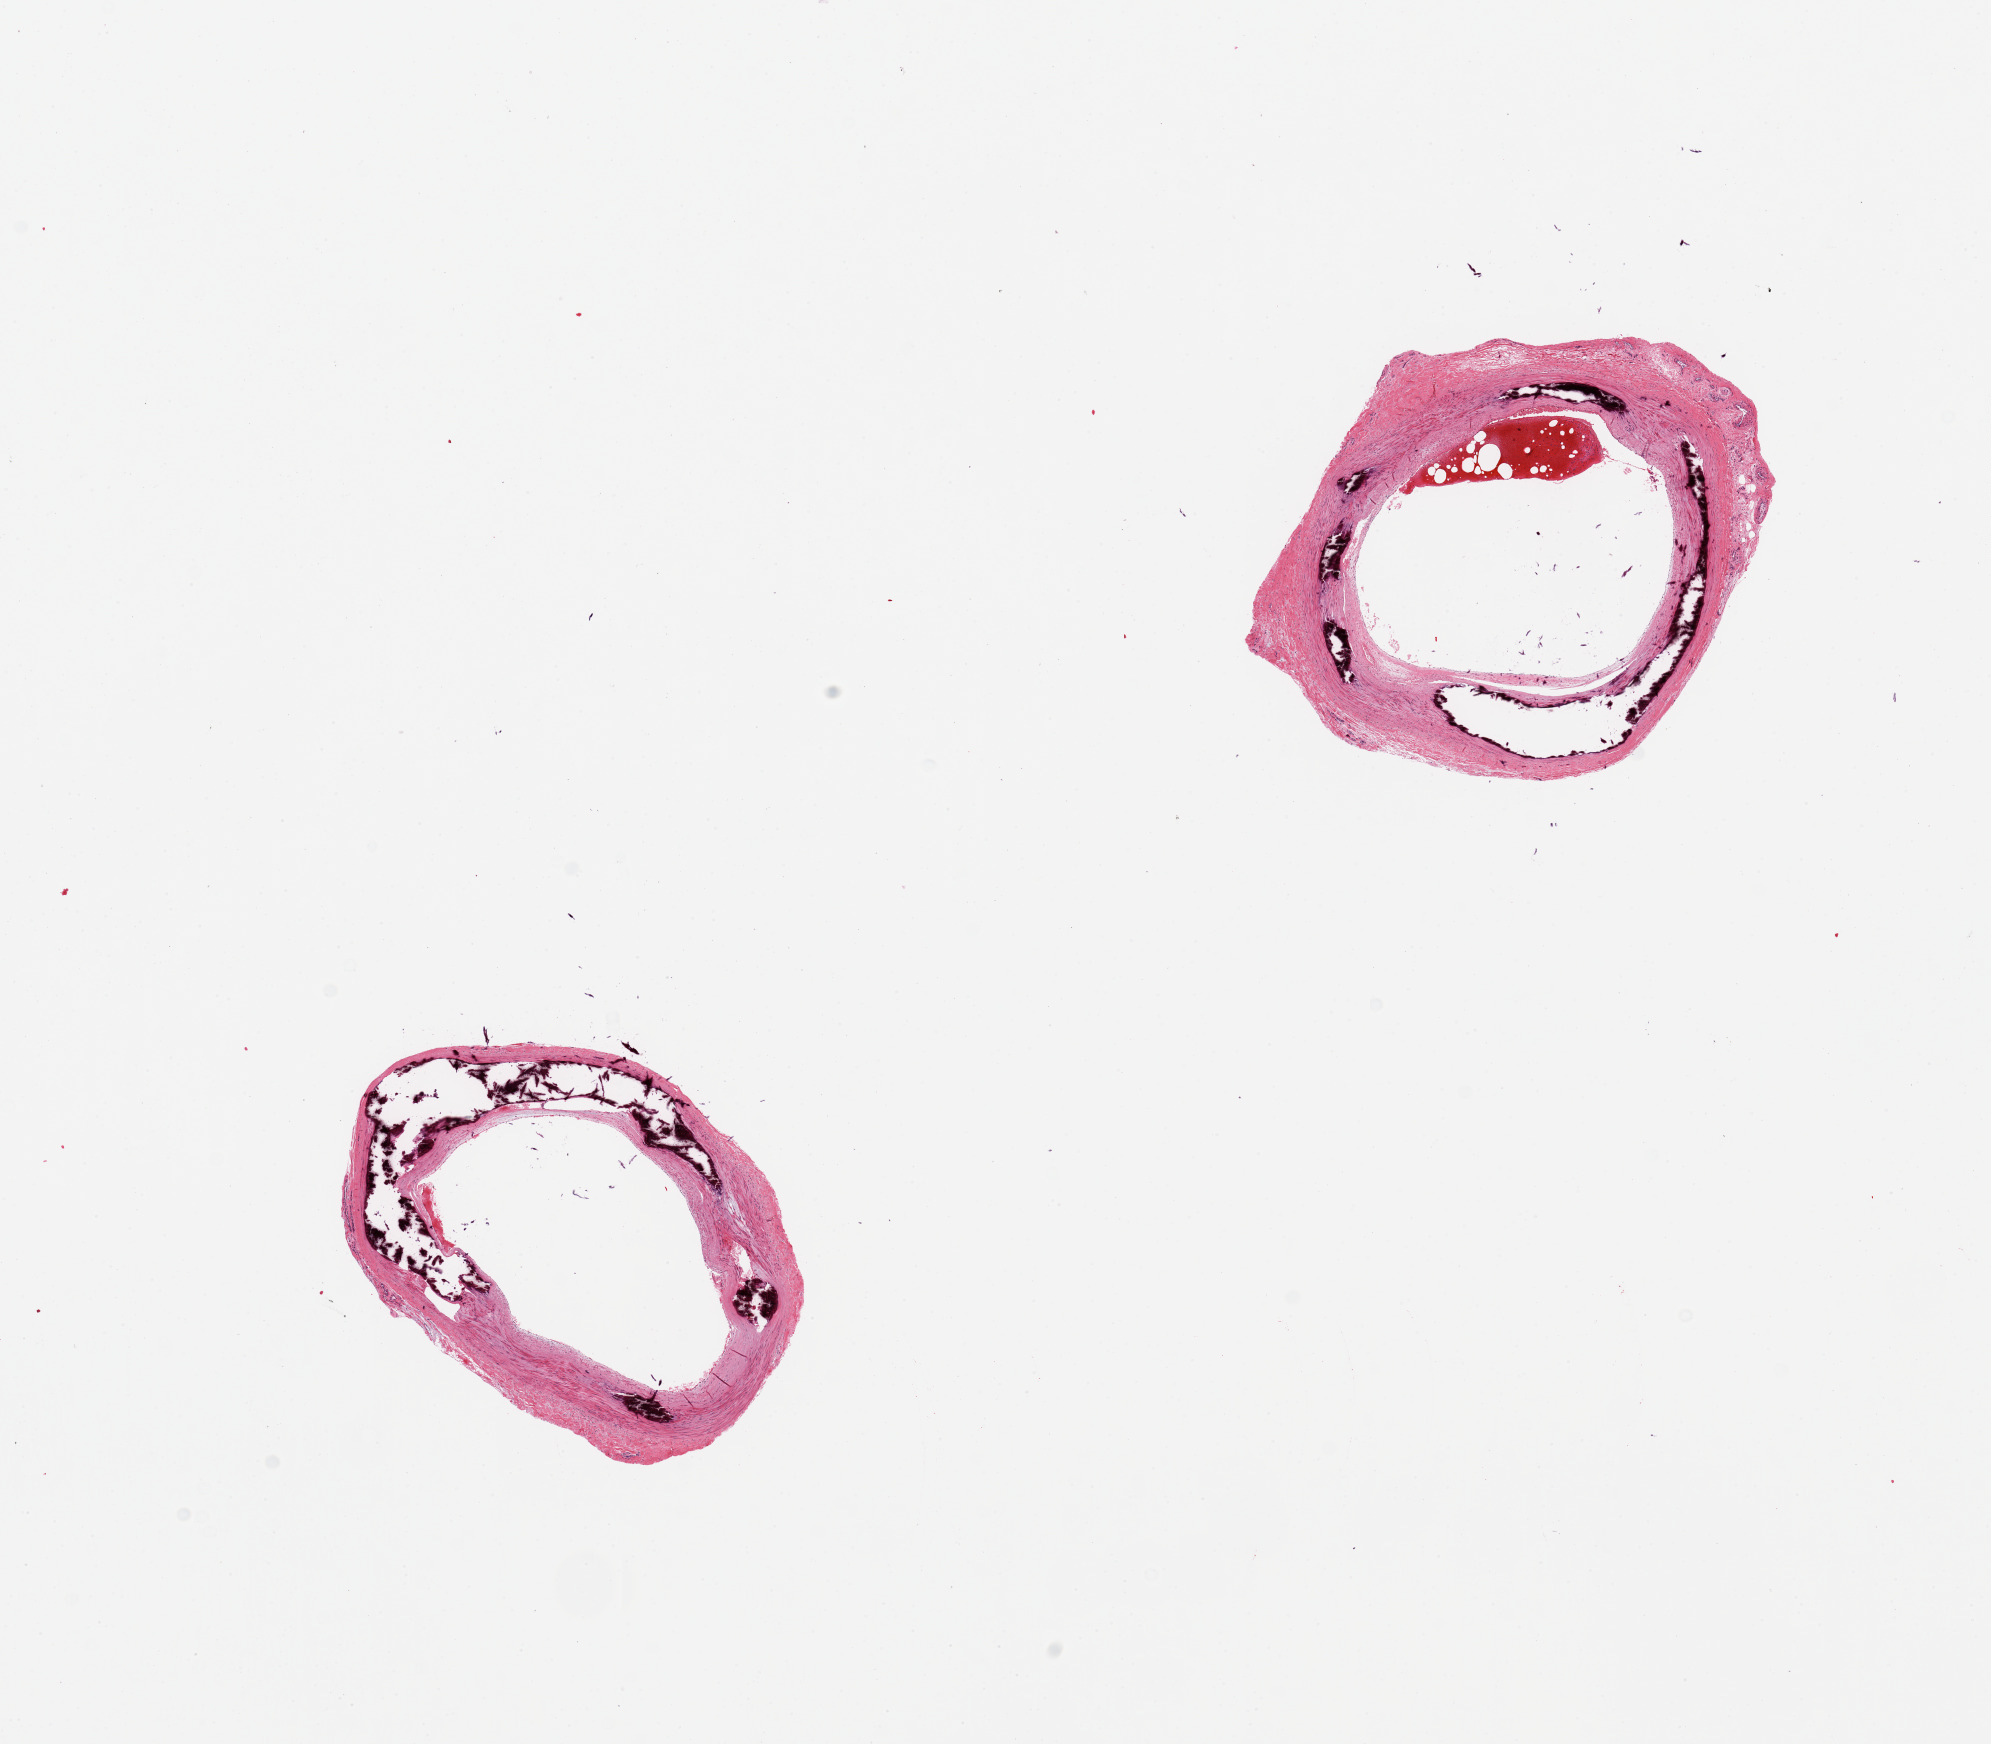
Hematoxylin and eosin (H&E) whole-slide image, brightfield, shown as a low-resolution overview of the whole scanned area (about 15.8 x 13.8 mm, slide scanned at 20x). PAXgene-fixed, paraffin-embedded tissue. Section of tibial artery (target tissue). Tissue donor sample. Donor: male.
Review note (as recorded): 2 pieces, clean specimens, prominent Monckeberg sclerosis.